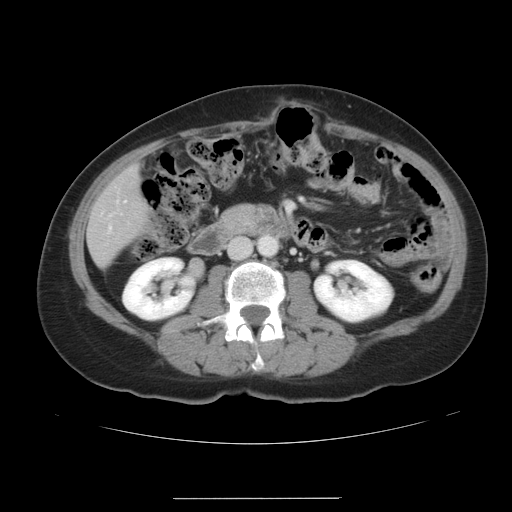
Contrast-enhanced abdominal CT, one axial slice; position 11 of 41 along the scan axis; intravenous contrast given; soft-tissue window (W 400 / L 40 HU); 5 mm slice thickness; 512 × 512 image matrix. Female patient, age 63 years. Case-level facts recorded for this patient, not image findings: diagnosis: colorectal cancer liver metastases, imaged before liver resection; multiple liver metastases: yes.
Outlined on this slice (outlined manually by an expert reader):
- liver: bounding box [x1, y1, x2, y2] px = [89, 167, 147, 265]
- planned liver remnant (the part of the liver to remain after resection): [89, 168, 148, 265]